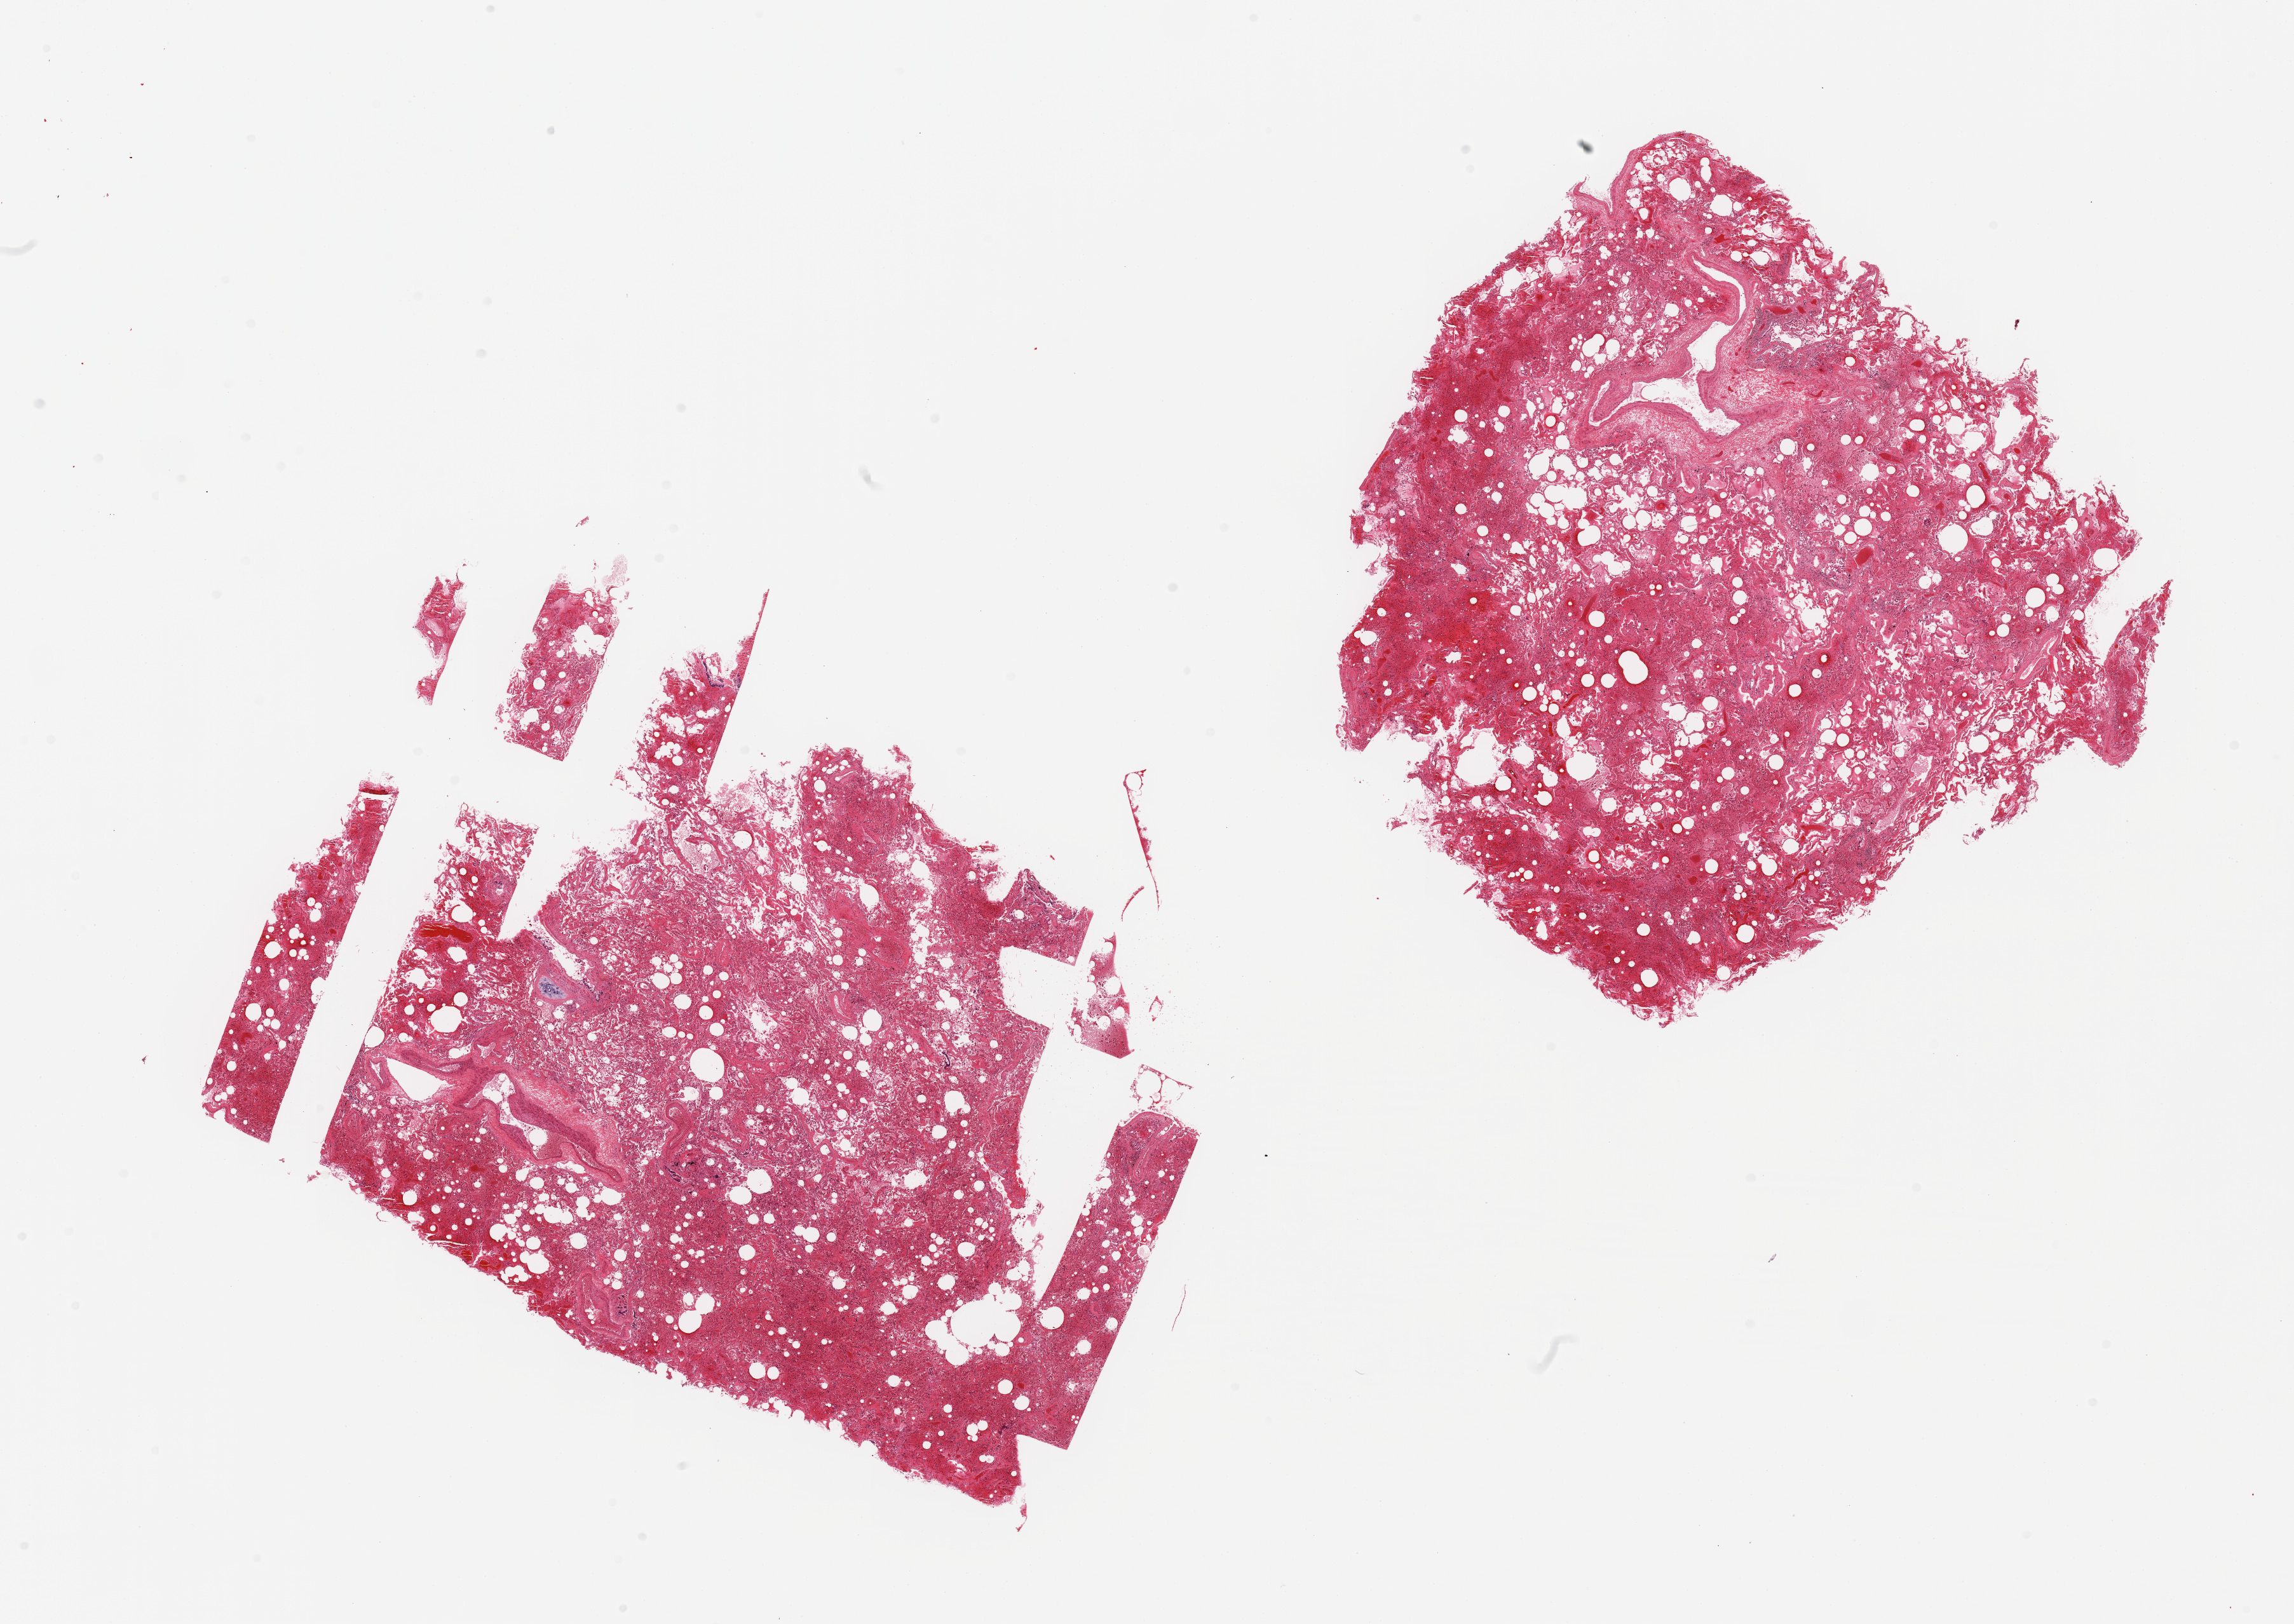
Whole-slide image, H&E stain — low-resolution overview of the scanned area, about 28.5 x 20.2 mm (acquisition: 20x scan), PAXgene-fixed, paraffin-embedded tissue, section of lung (target tissue), tissue donor sample. Male donor.
Review note (as recorded): 2 pieces; 60% hemorrhage (consistent with pulmonary embolism); patchy fibrosis.